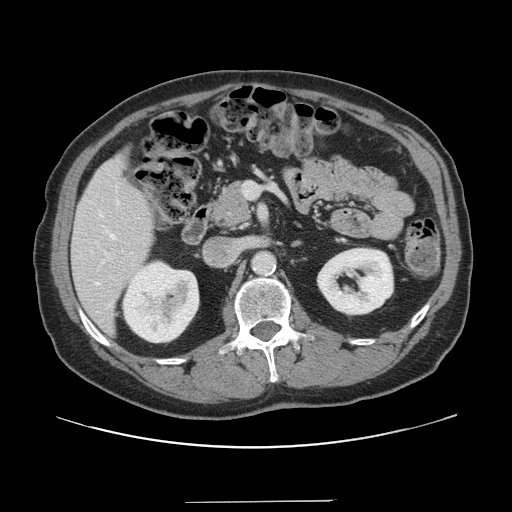
Contrast-enhanced abdominal CT, one axial slice; slice 69 of 151 in the series (ordered by position); 120 kVp; intravenous contrast given; soft-tissue window (W 400 / L 40 HU); 512 × 512 image matrix. Male patient, age 63 years. Case-level facts recorded for this patient, not image findings: diagnosis: colorectal cancer liver metastases, imaged before liver resection; multiple liver metastases: no; largest metastasis: 2.1 cm.
Annotated regions visible in this slice (outlined manually by an expert reader):
- hepatic veins: bounding box [x1, y1, x2, y2] px = [95, 202, 119, 285]
- liver: [73, 152, 154, 332]
- planned liver remnant (the part of the liver to remain after resection): [72, 153, 154, 333]
- portal vein (with intrahepatic branches): [101, 182, 258, 264]